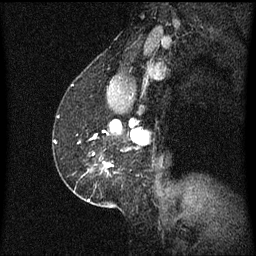
Breast MRI (dynamic contrast-enhanced), one sagittal slice. Slice 39 of 60 in the series (ordered by position). Dynamic contrast-enhanced series, image 2 of 3 at this slice position (ordered by acquisition). 1.5 T. TE 4.2 ms, TR 8.4 ms. 2 mm slice thickness. 256 × 256 image matrix, field of view 200 × 200 mm. Female patient, age 52 years. From the clinical record (not read from this slice): setting: breast cancer imaged before/during neoadjuvant chemotherapy; receptor status: HER2-positive.
Structures marked on this image (semi-automatic segmentation, software-assisted and operator-edited):
- analysis volume of interest (the breast-tissue region the enhancement analysis was run in; not a lesion): bounding box [x1, y1, x2, y2] px = [65, 158, 114, 203]
- tumour enhancement mask (voxels above the 70 % enhancement threshold inside the analysis volume of interest): [104, 162, 112, 167]